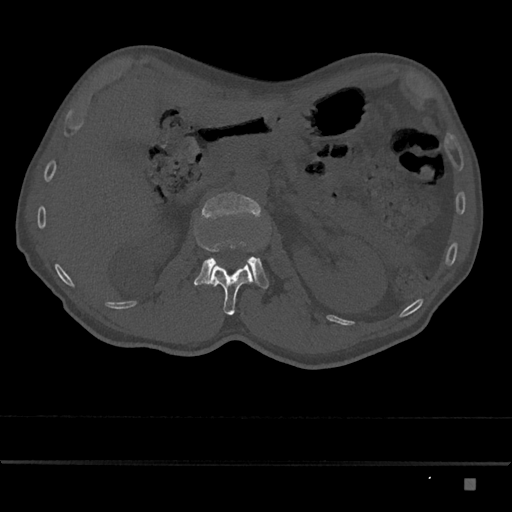
CT including the spine, one axial slice. Slice 517 of 797 in the series (ordered by position). 120 kVp. Bone window (W 1800 / L 400 HU). 512 × 512 image matrix, field of view 390 × 390 mm. Male patient, age 72 years. Case-level facts recorded for this patient, not image findings: primary cancer: prostate.
Annotated regions visible in this slice (semi-automatic segmentation, software-assisted and operator-edited):
- L1 vertebra: box from (x=208, y=262) to (x=255, y=315) px
- L2 vertebra: (x=194, y=192)–(x=269, y=289)